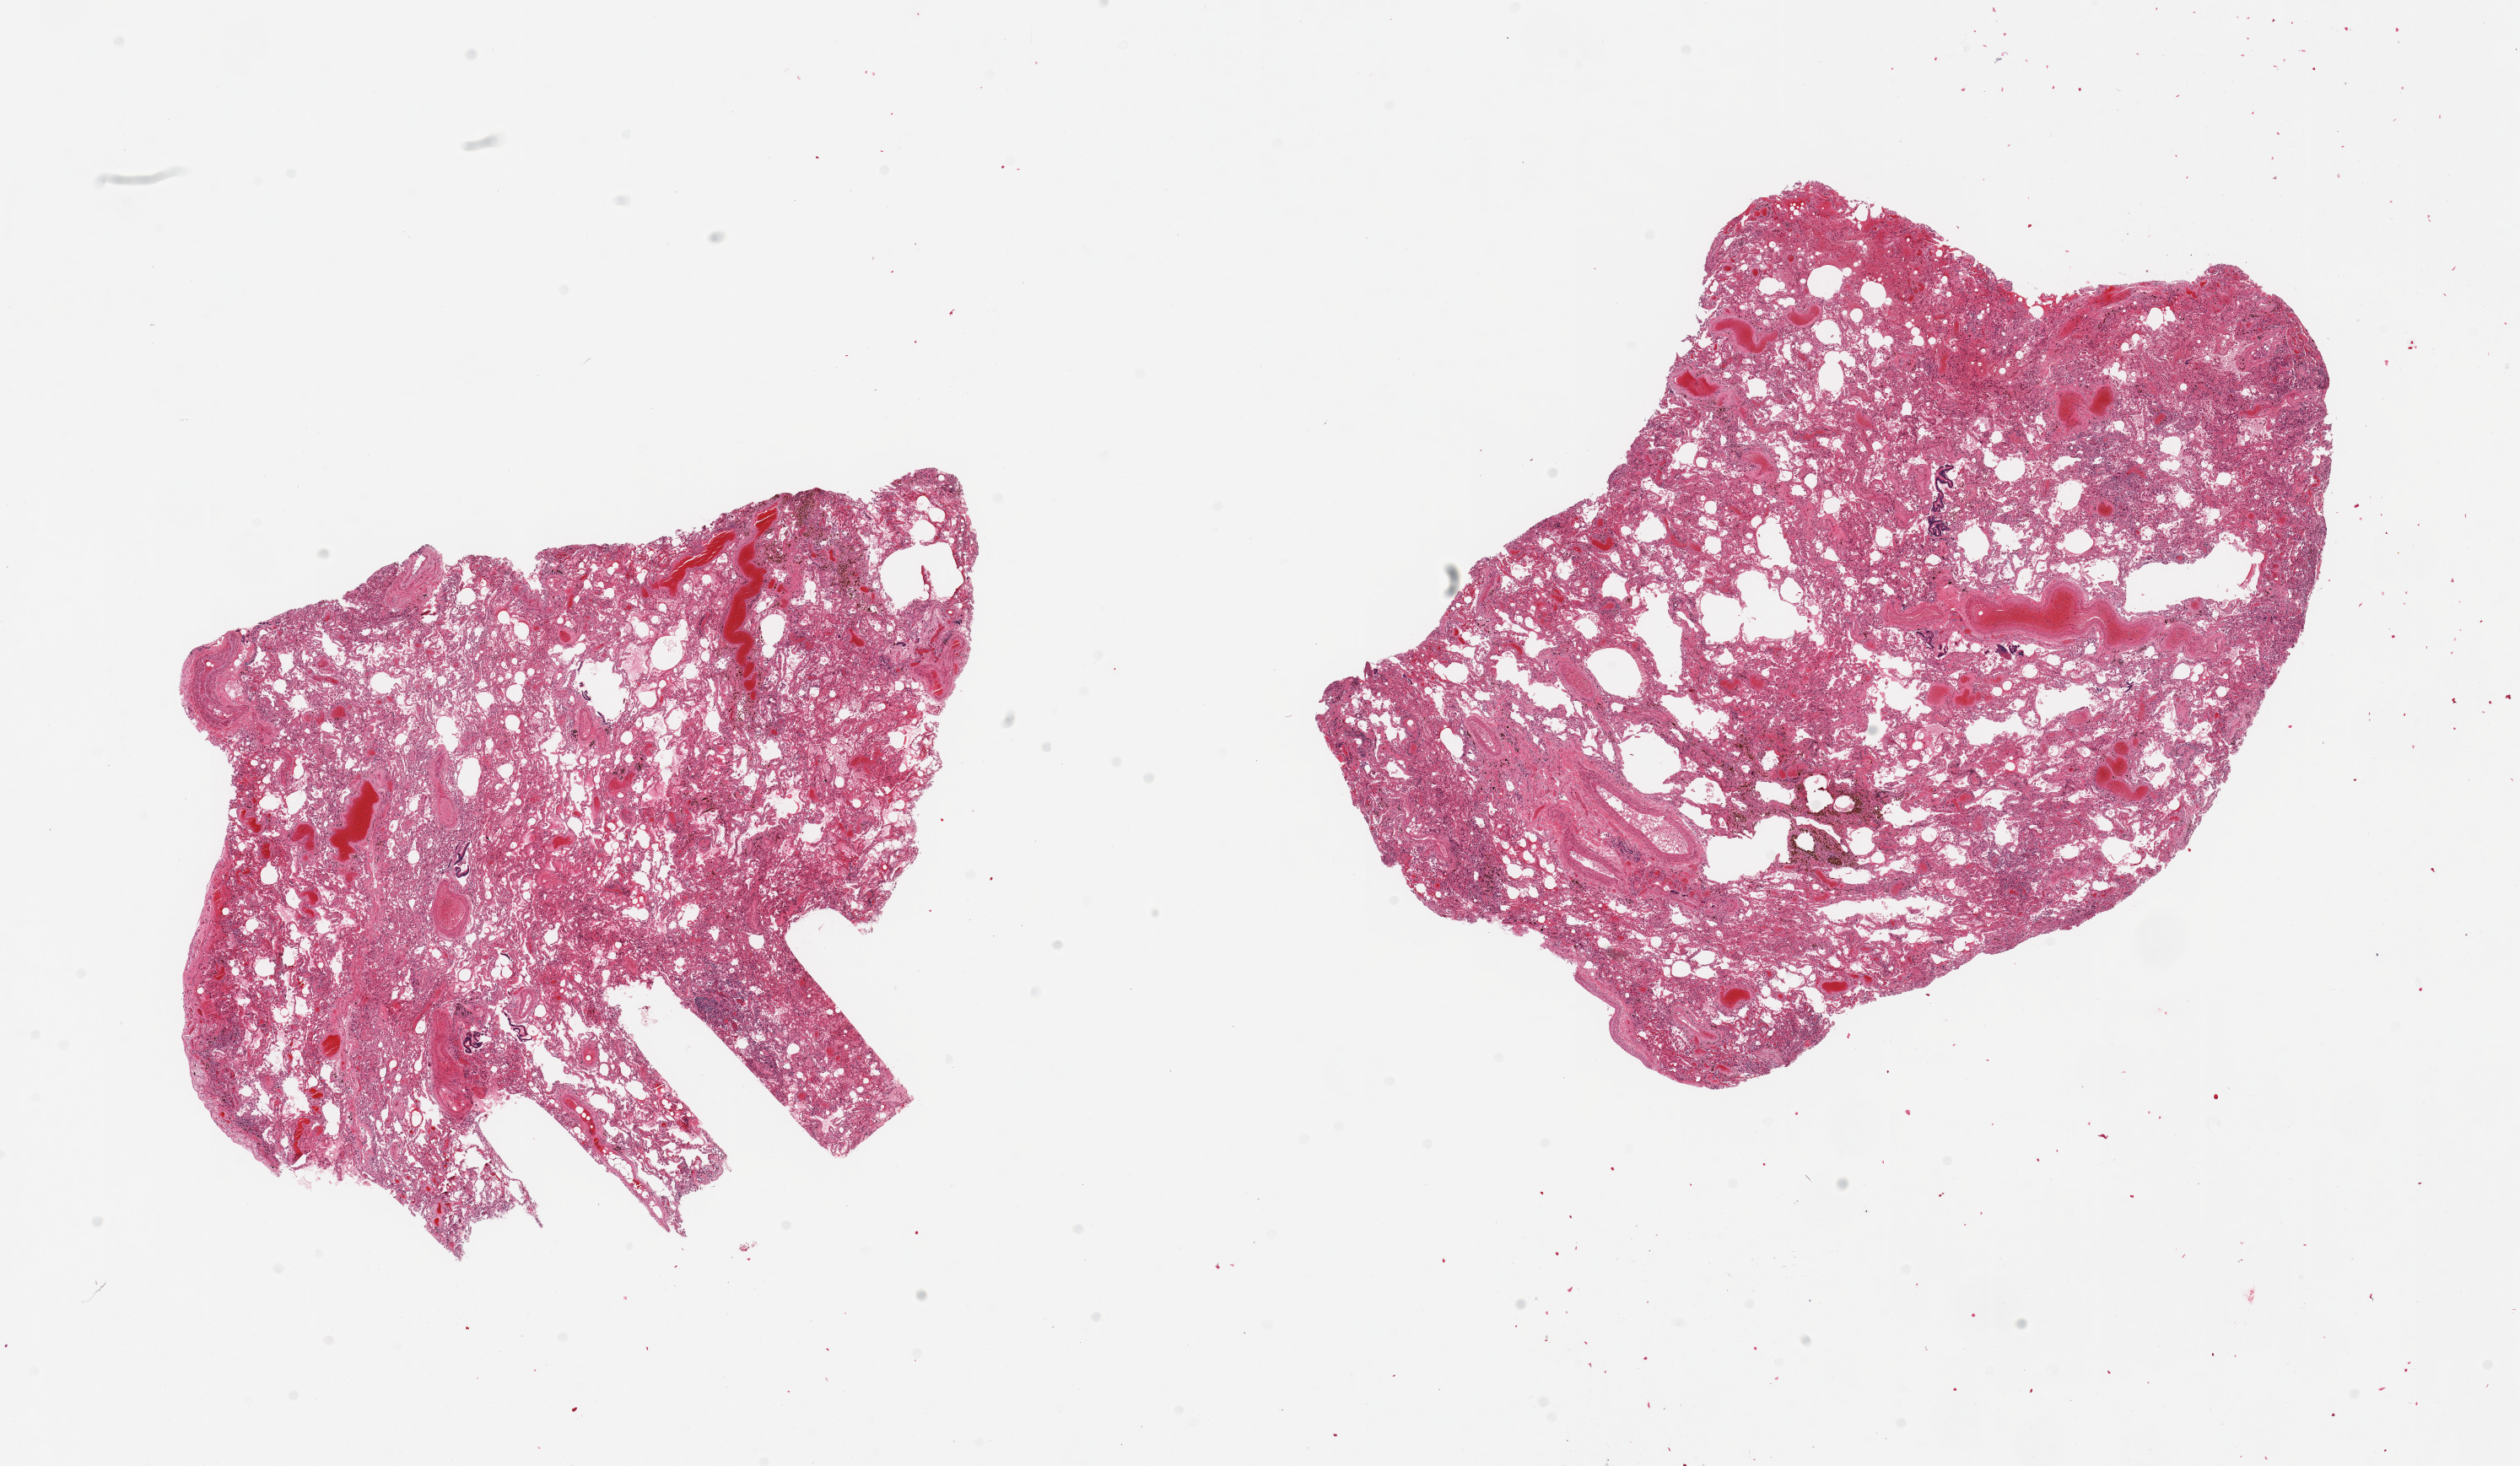
Digitized hematoxylin and eosin (H&E)-stained section — whole scanned area (about 23.6 x 13.7 mm, acquisition: 20x scan) shown as a low-resolution overview; PAXgene-fixed, paraffin-embedded tissue; sampled site (target tissue): lung; donor tissue sample.
Pathologist's review note for this sample: 2 pieces, moderate-marked chronic congestion, peripheral bronchial metaplasia.